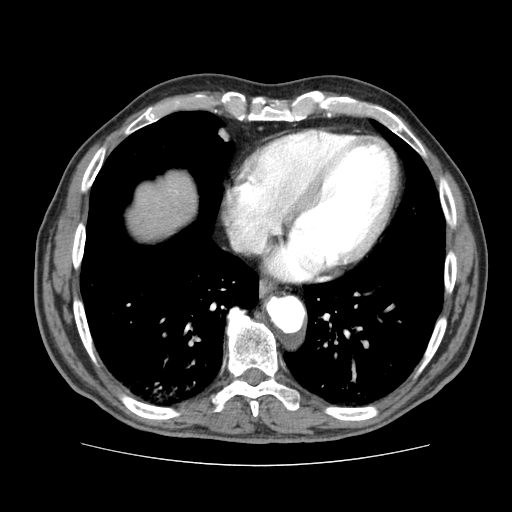
Contrast-enhanced abdominal CT (liver protocol), one axial slice; position 75 of 79 along the scan axis; reconstruction kernel STANDARD; soft-tissue window (W 400 / L 40 HU); 2.5 mm slice thickness; 512 × 512 image matrix, field of view 360 × 360 mm. Case-level facts recorded for this patient, not image findings: diagnosis: hepatocellular carcinoma (patient treated with transarterial chemoembolisation; whether this scan precedes or follows treatment is not stated here); TNM stage (as recorded): Stage-I; Child-Pugh class: A; tumour nodularity: uninodular.
Structures marked on this image (semi-automatically segmented with operator editing):
- abdominal aorta: bounding box <267,296,305,333> (left, top, right, bottom; pixels)
- liver parenchyma outside the tumour (the mass and vessels are separate outlines, so this box may not span the whole liver): <132,176,194,236>